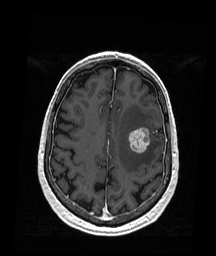
Brain MRI from a brain-tumour surgery series, one axial slice. Slice 59 of 176 in the series (ordered by position). T1-weighted post-contrast. 1 mm slice thickness. 216 × 256 image matrix, field of view 211 × 250 mm. From the clinical record (not read from this slice): histopathology: Metastatic Melanoma.
Outlined on this slice (expert manual segmentation):
- tumour: bounding box (x1, y1, x2, y2) in pixels: (128, 128, 151, 153)